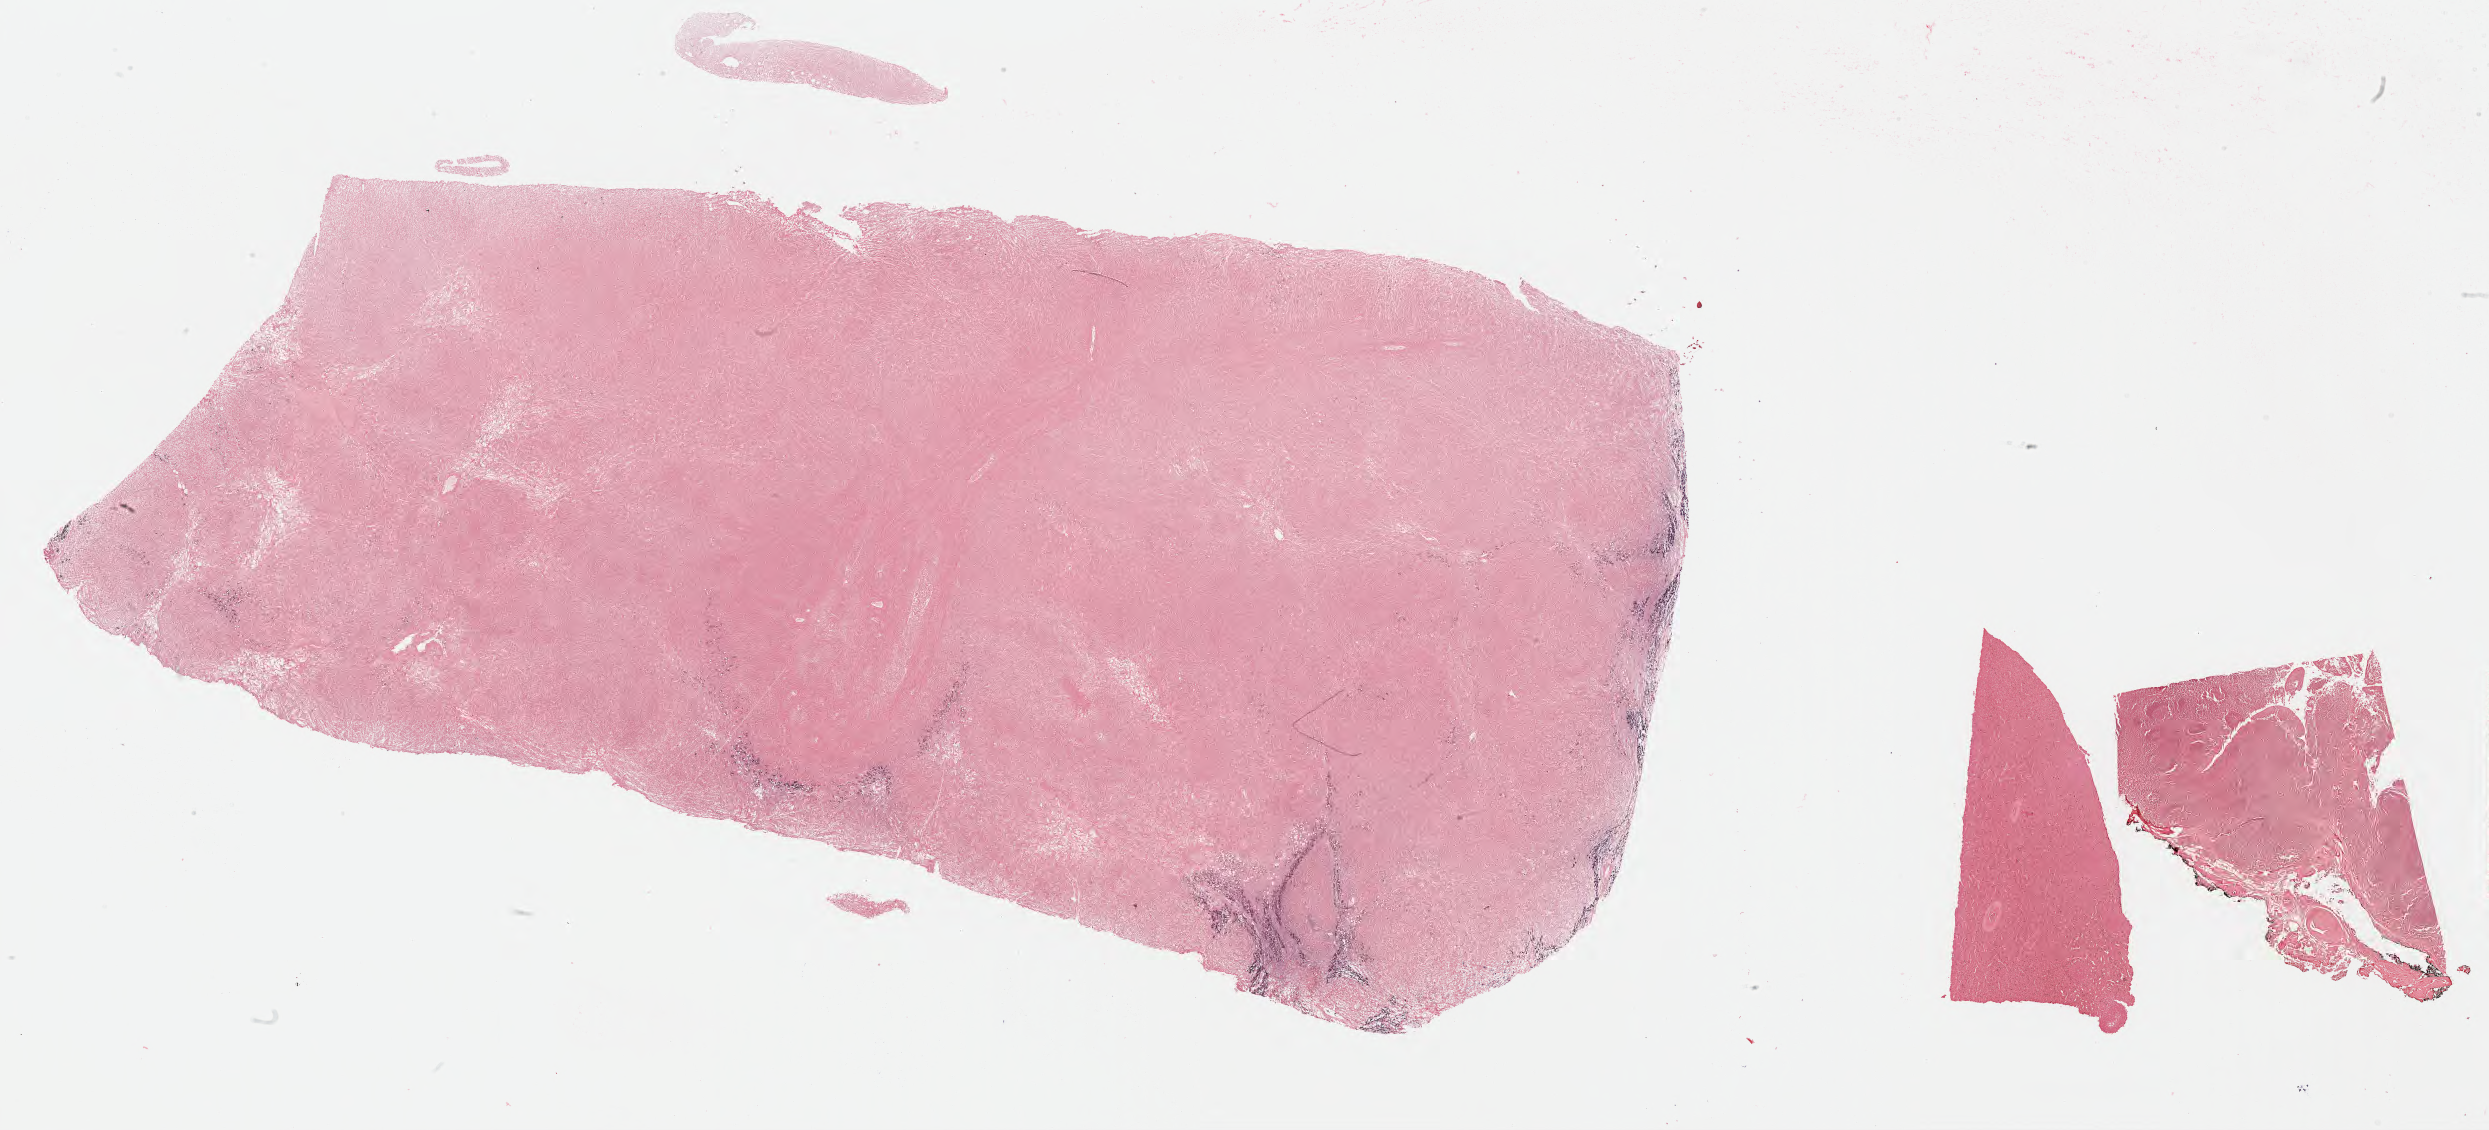
Whole-slide image, Epstein–Barr virus-encoded RNA (EBER) in-situ hybridisation, a low-resolution overview of the entire scanned area, about 40.3 x 18.3 mm, specimen: tumor tissue. Male patient, aged 39.
Diagnosis: Diffuse large B-cell lymphoma, NOS.